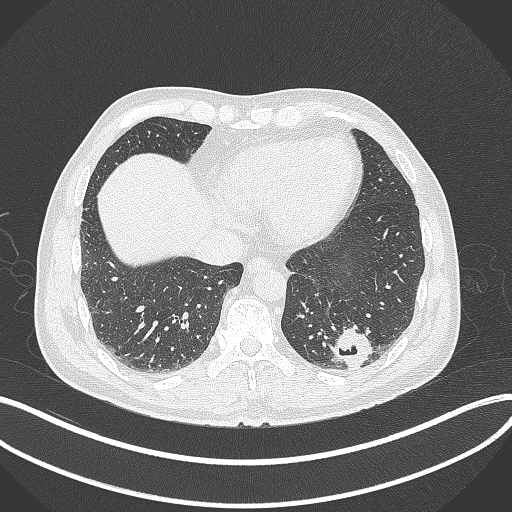
Chest CT, one axial slice; 120 kVp; lung window (W 1500 / L -600 HU); 1 mm slice thickness; 512 × 512 image matrix, field of view 400 × 400 mm. Patient: male, 54 years. Case-level facts recorded for this patient, not image findings: clinical TNM (as recorded): T1c N0 M1; histopathological grade: G3.
Outlined on this slice (rectangle marked by the reading radiologist):
- lung tumour (recorded histology: adenocarcinoma): bounding box [x1, y1, x2, y2] px = [326, 325, 374, 371]